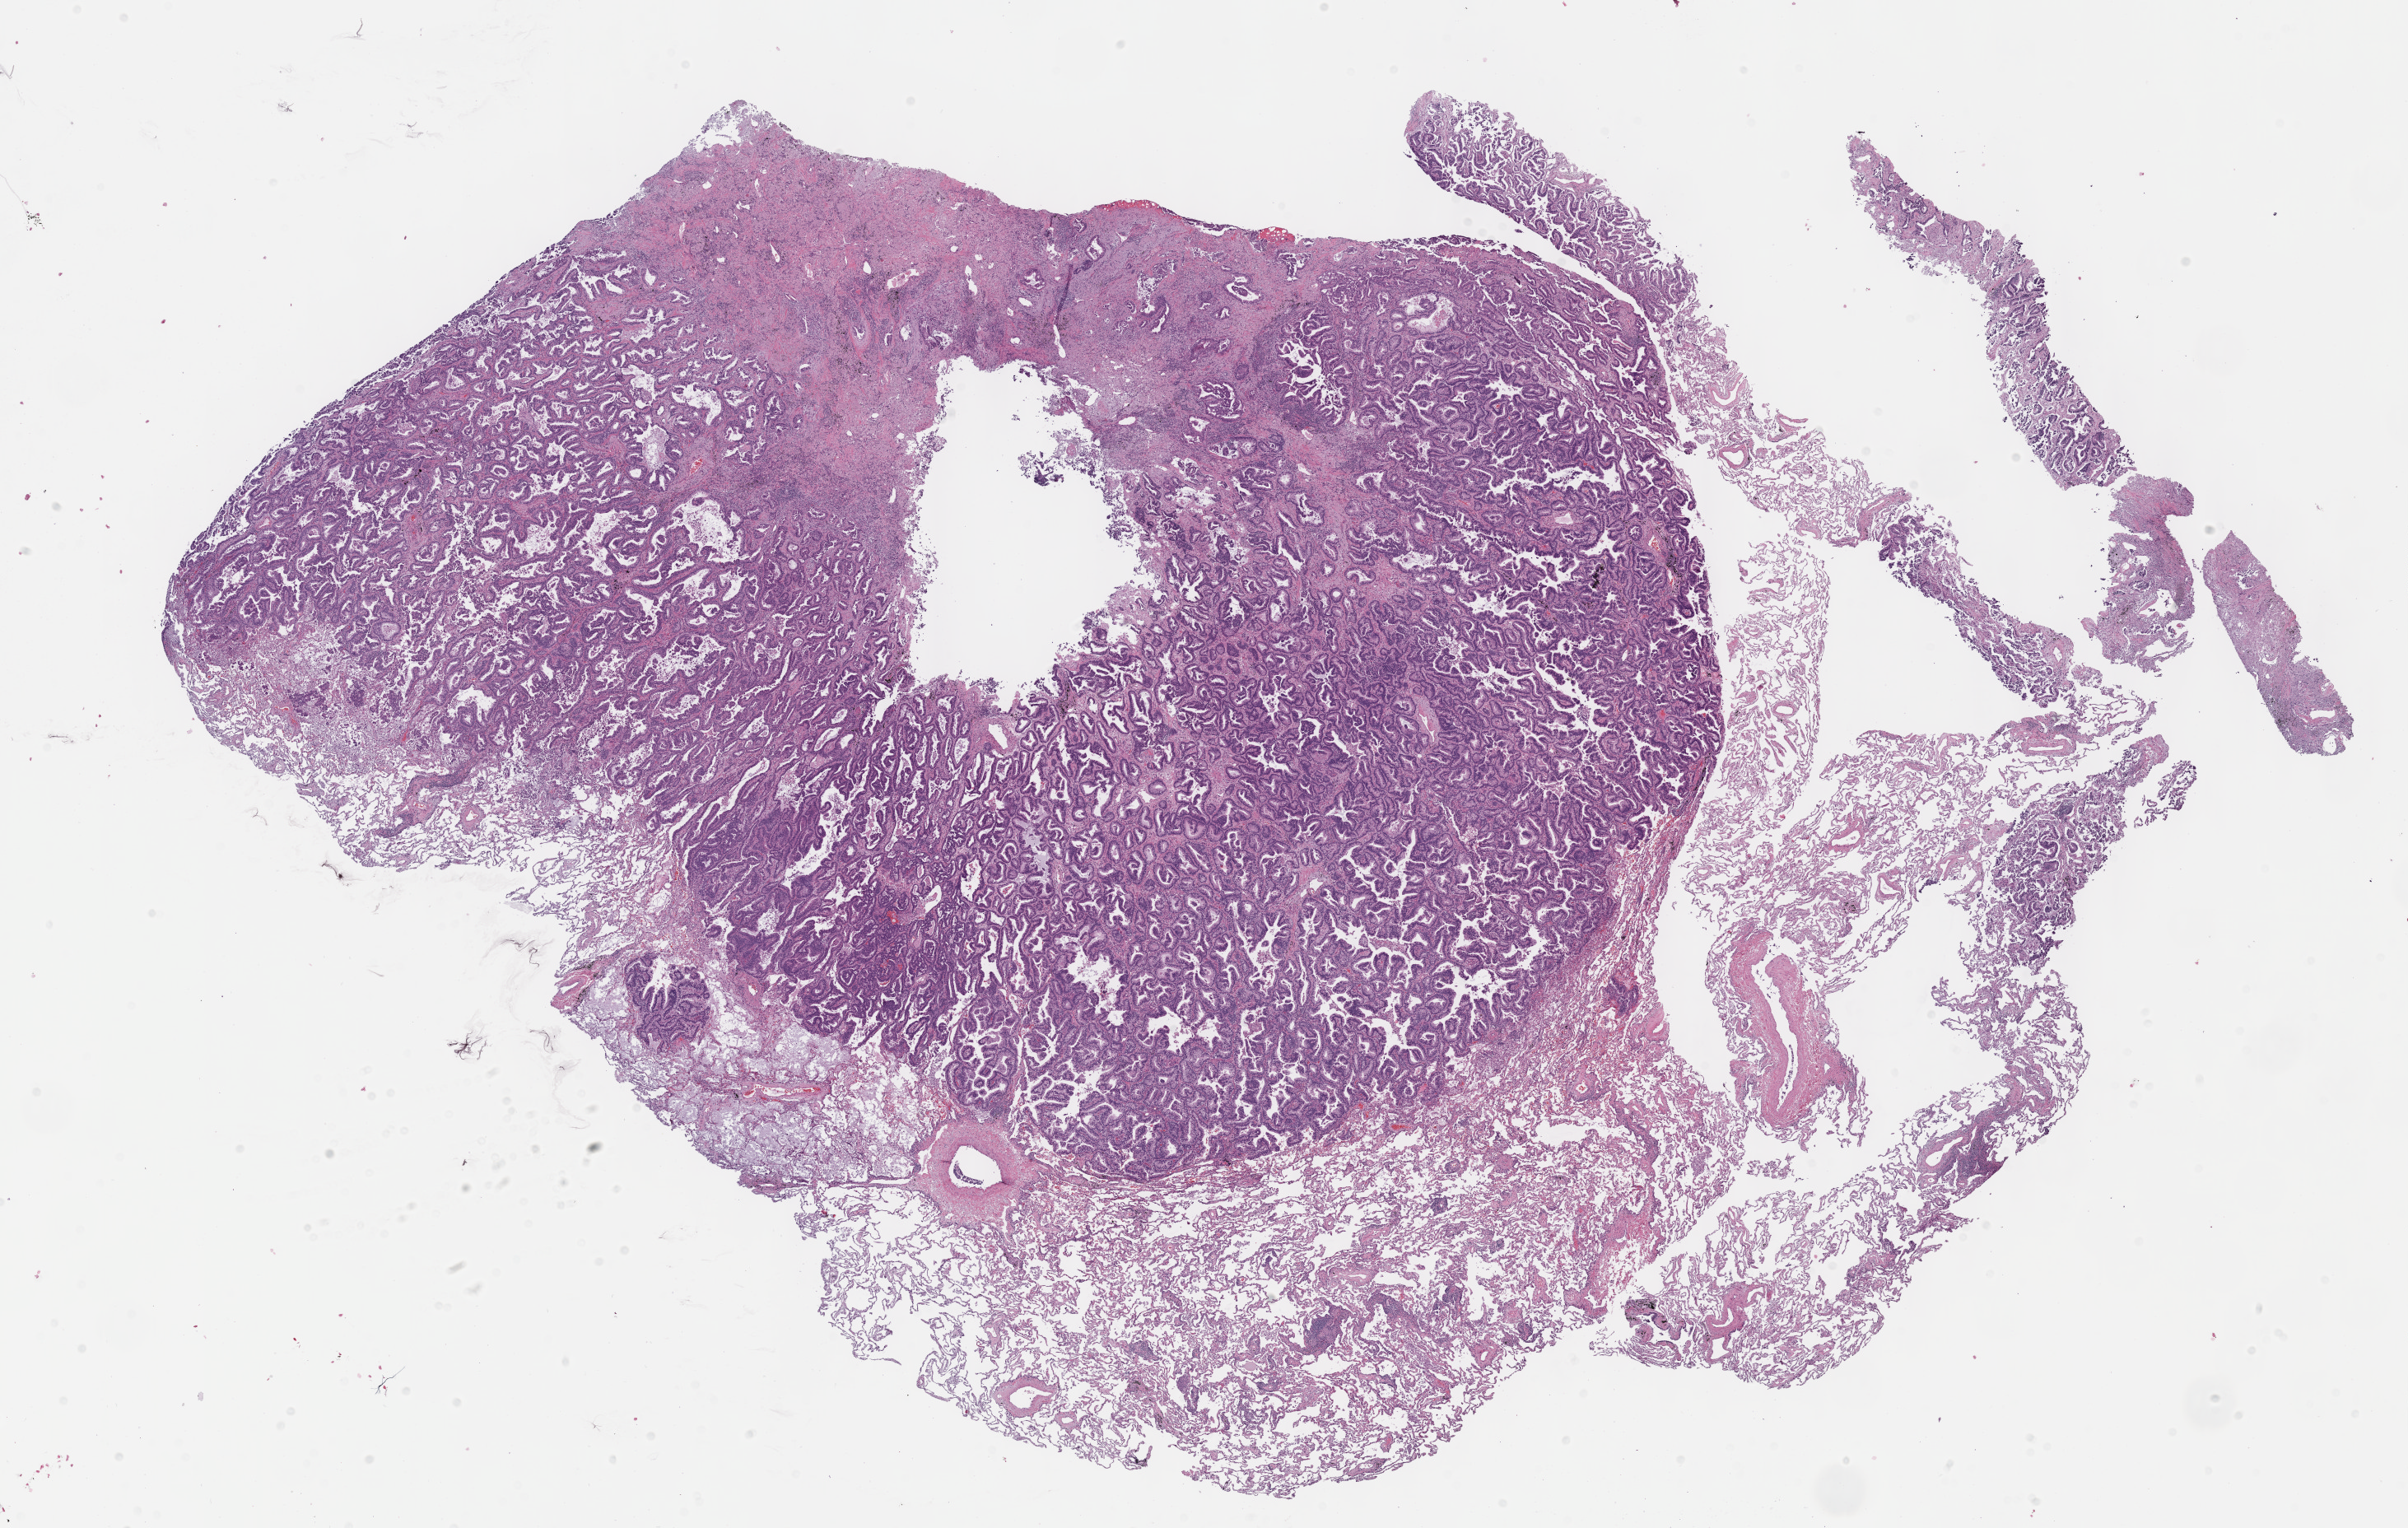
Digitized H&E-stained tissue section (whole slide), shown as a low-resolution overview of the whole scanned area (about 23.6 x 15.0 mm, from a 40x scan), formalin-fixed paraffin-embedded (FFPE) diagnostic section, sample: primary tumour, lung. Patient: female, age at initial diagnosis 76 years.
• AJCC pathologic stage: IB
• pathologic diagnosis: Adenocarcinoma, NOS (upper lobe, lung)
• laterality: left